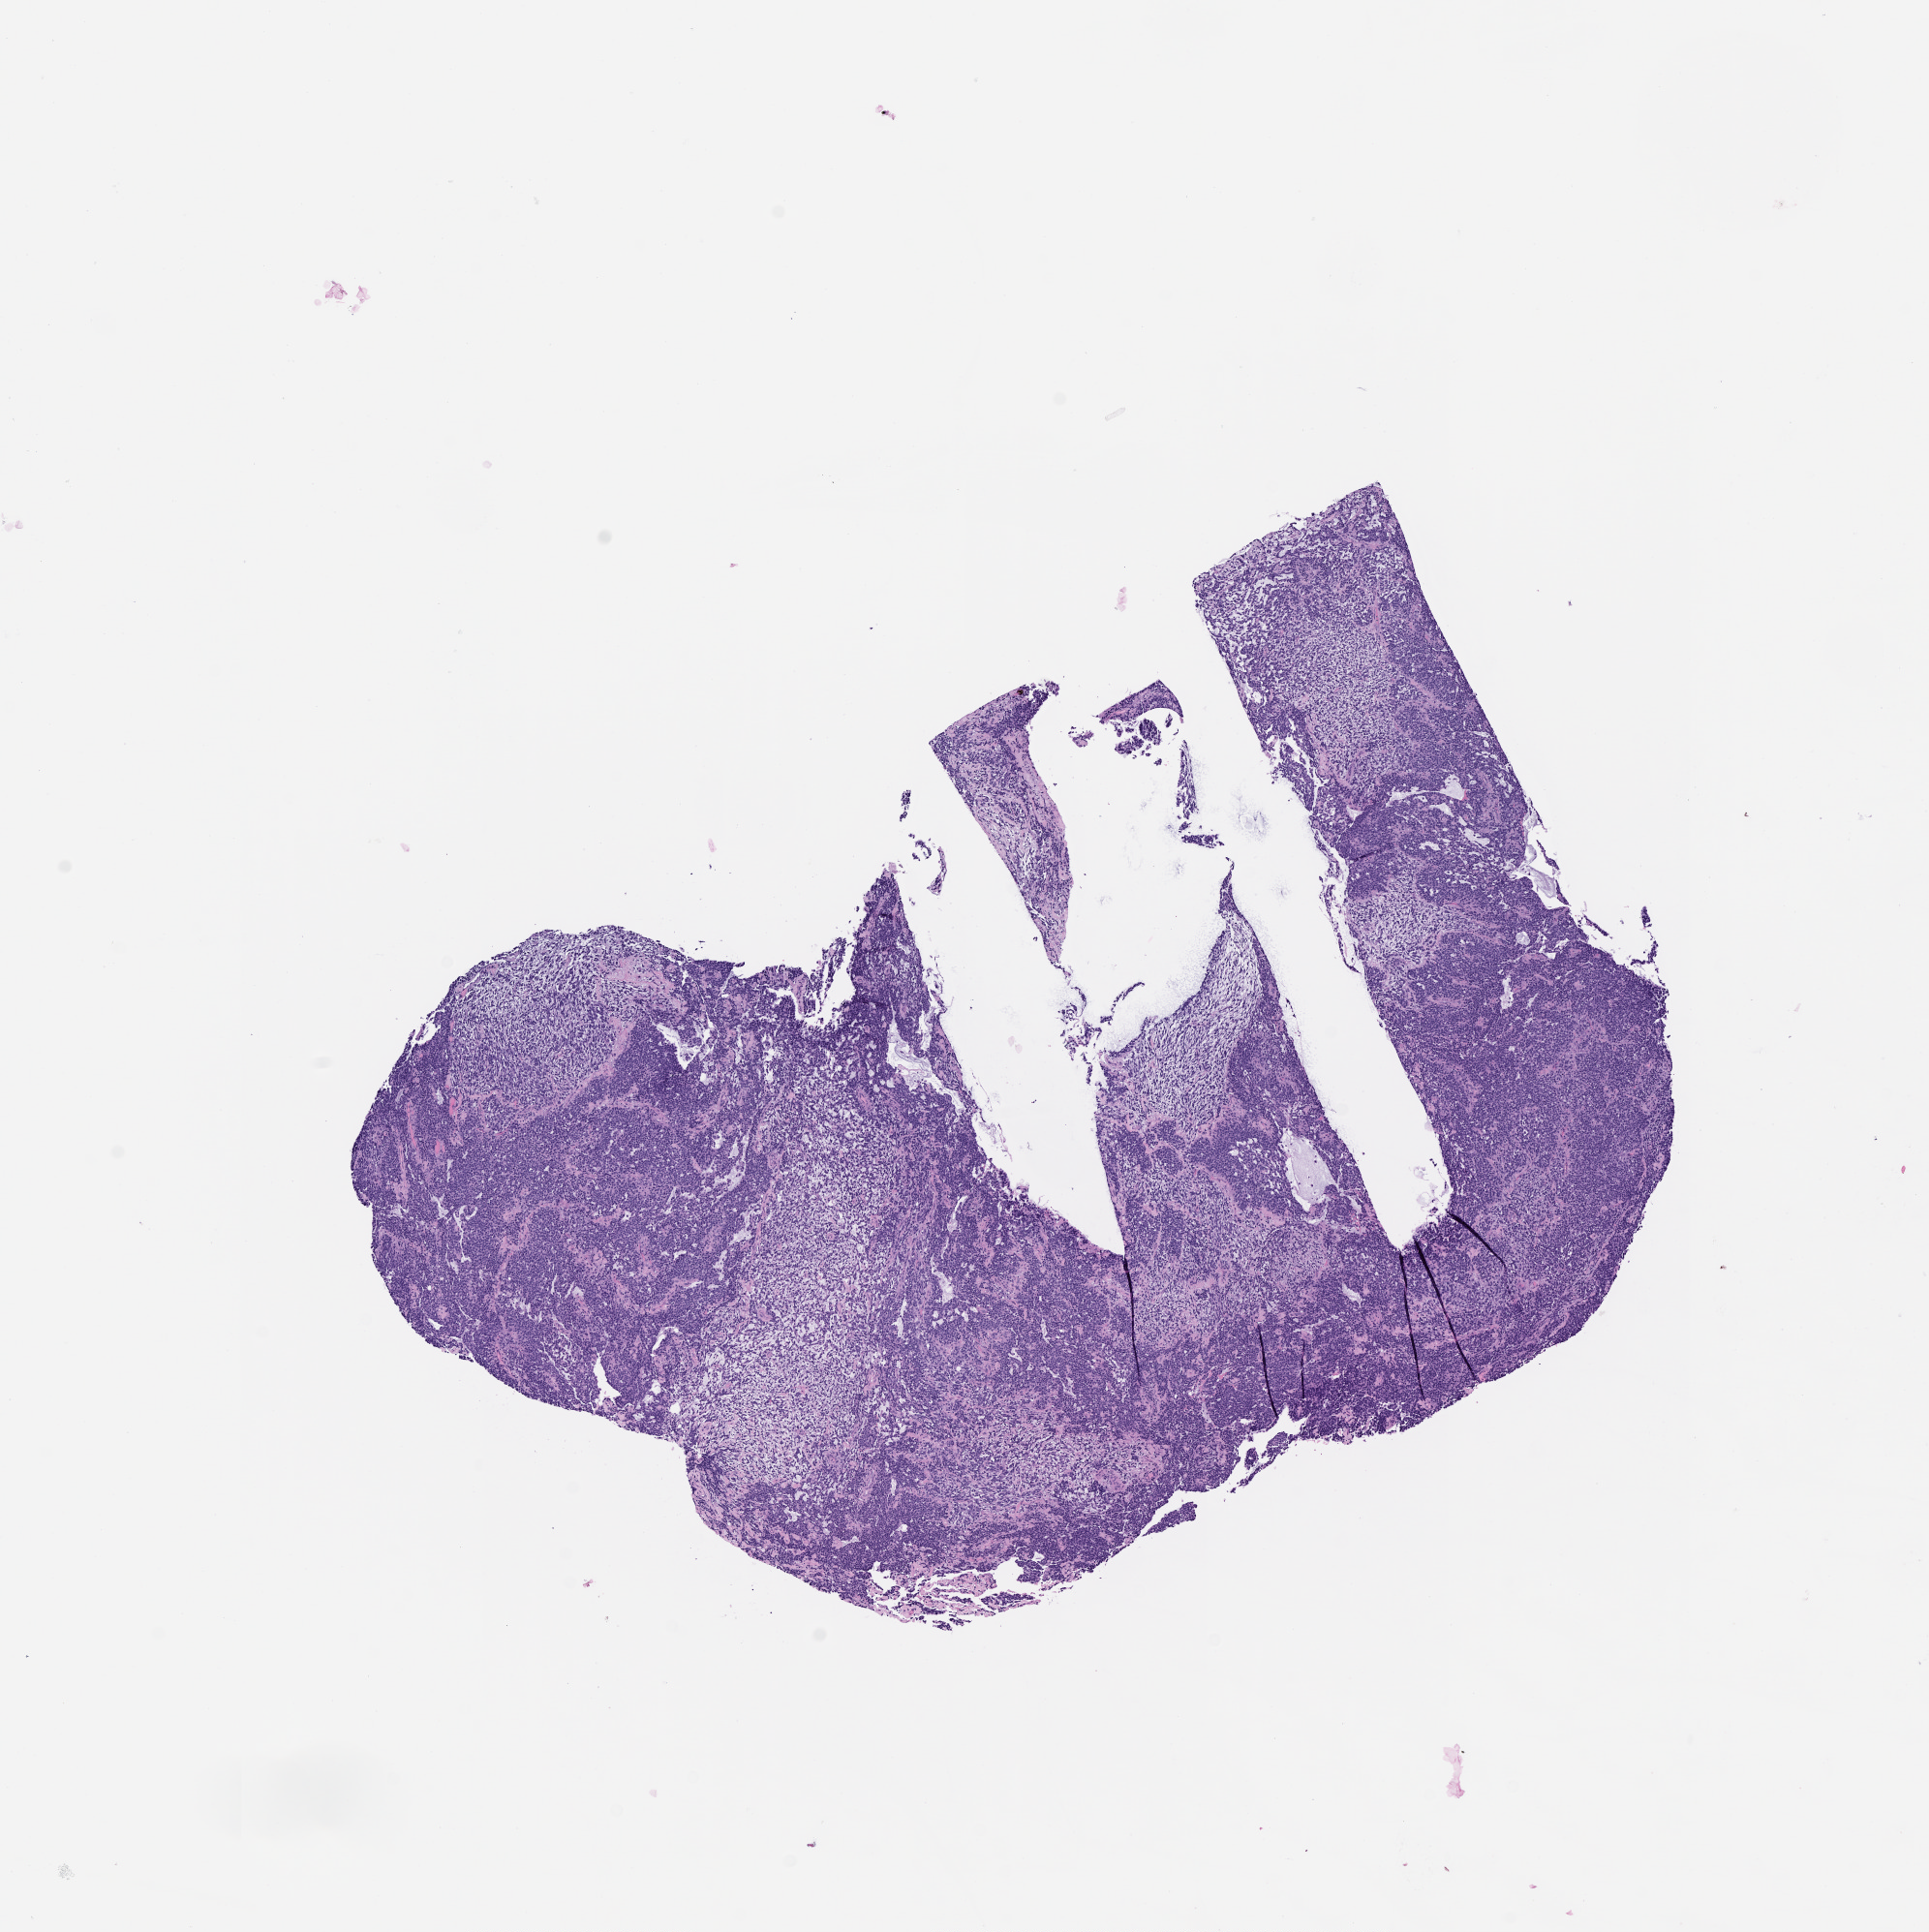
Whole-slide histology image, H&E — a low-resolution overview of the entire scanned area, about 8.0 x 8.0 mm (slide scanned at 20x).
• patient diagnosis (cohort enrolment): sarcoma (site not recorded at cohort level)